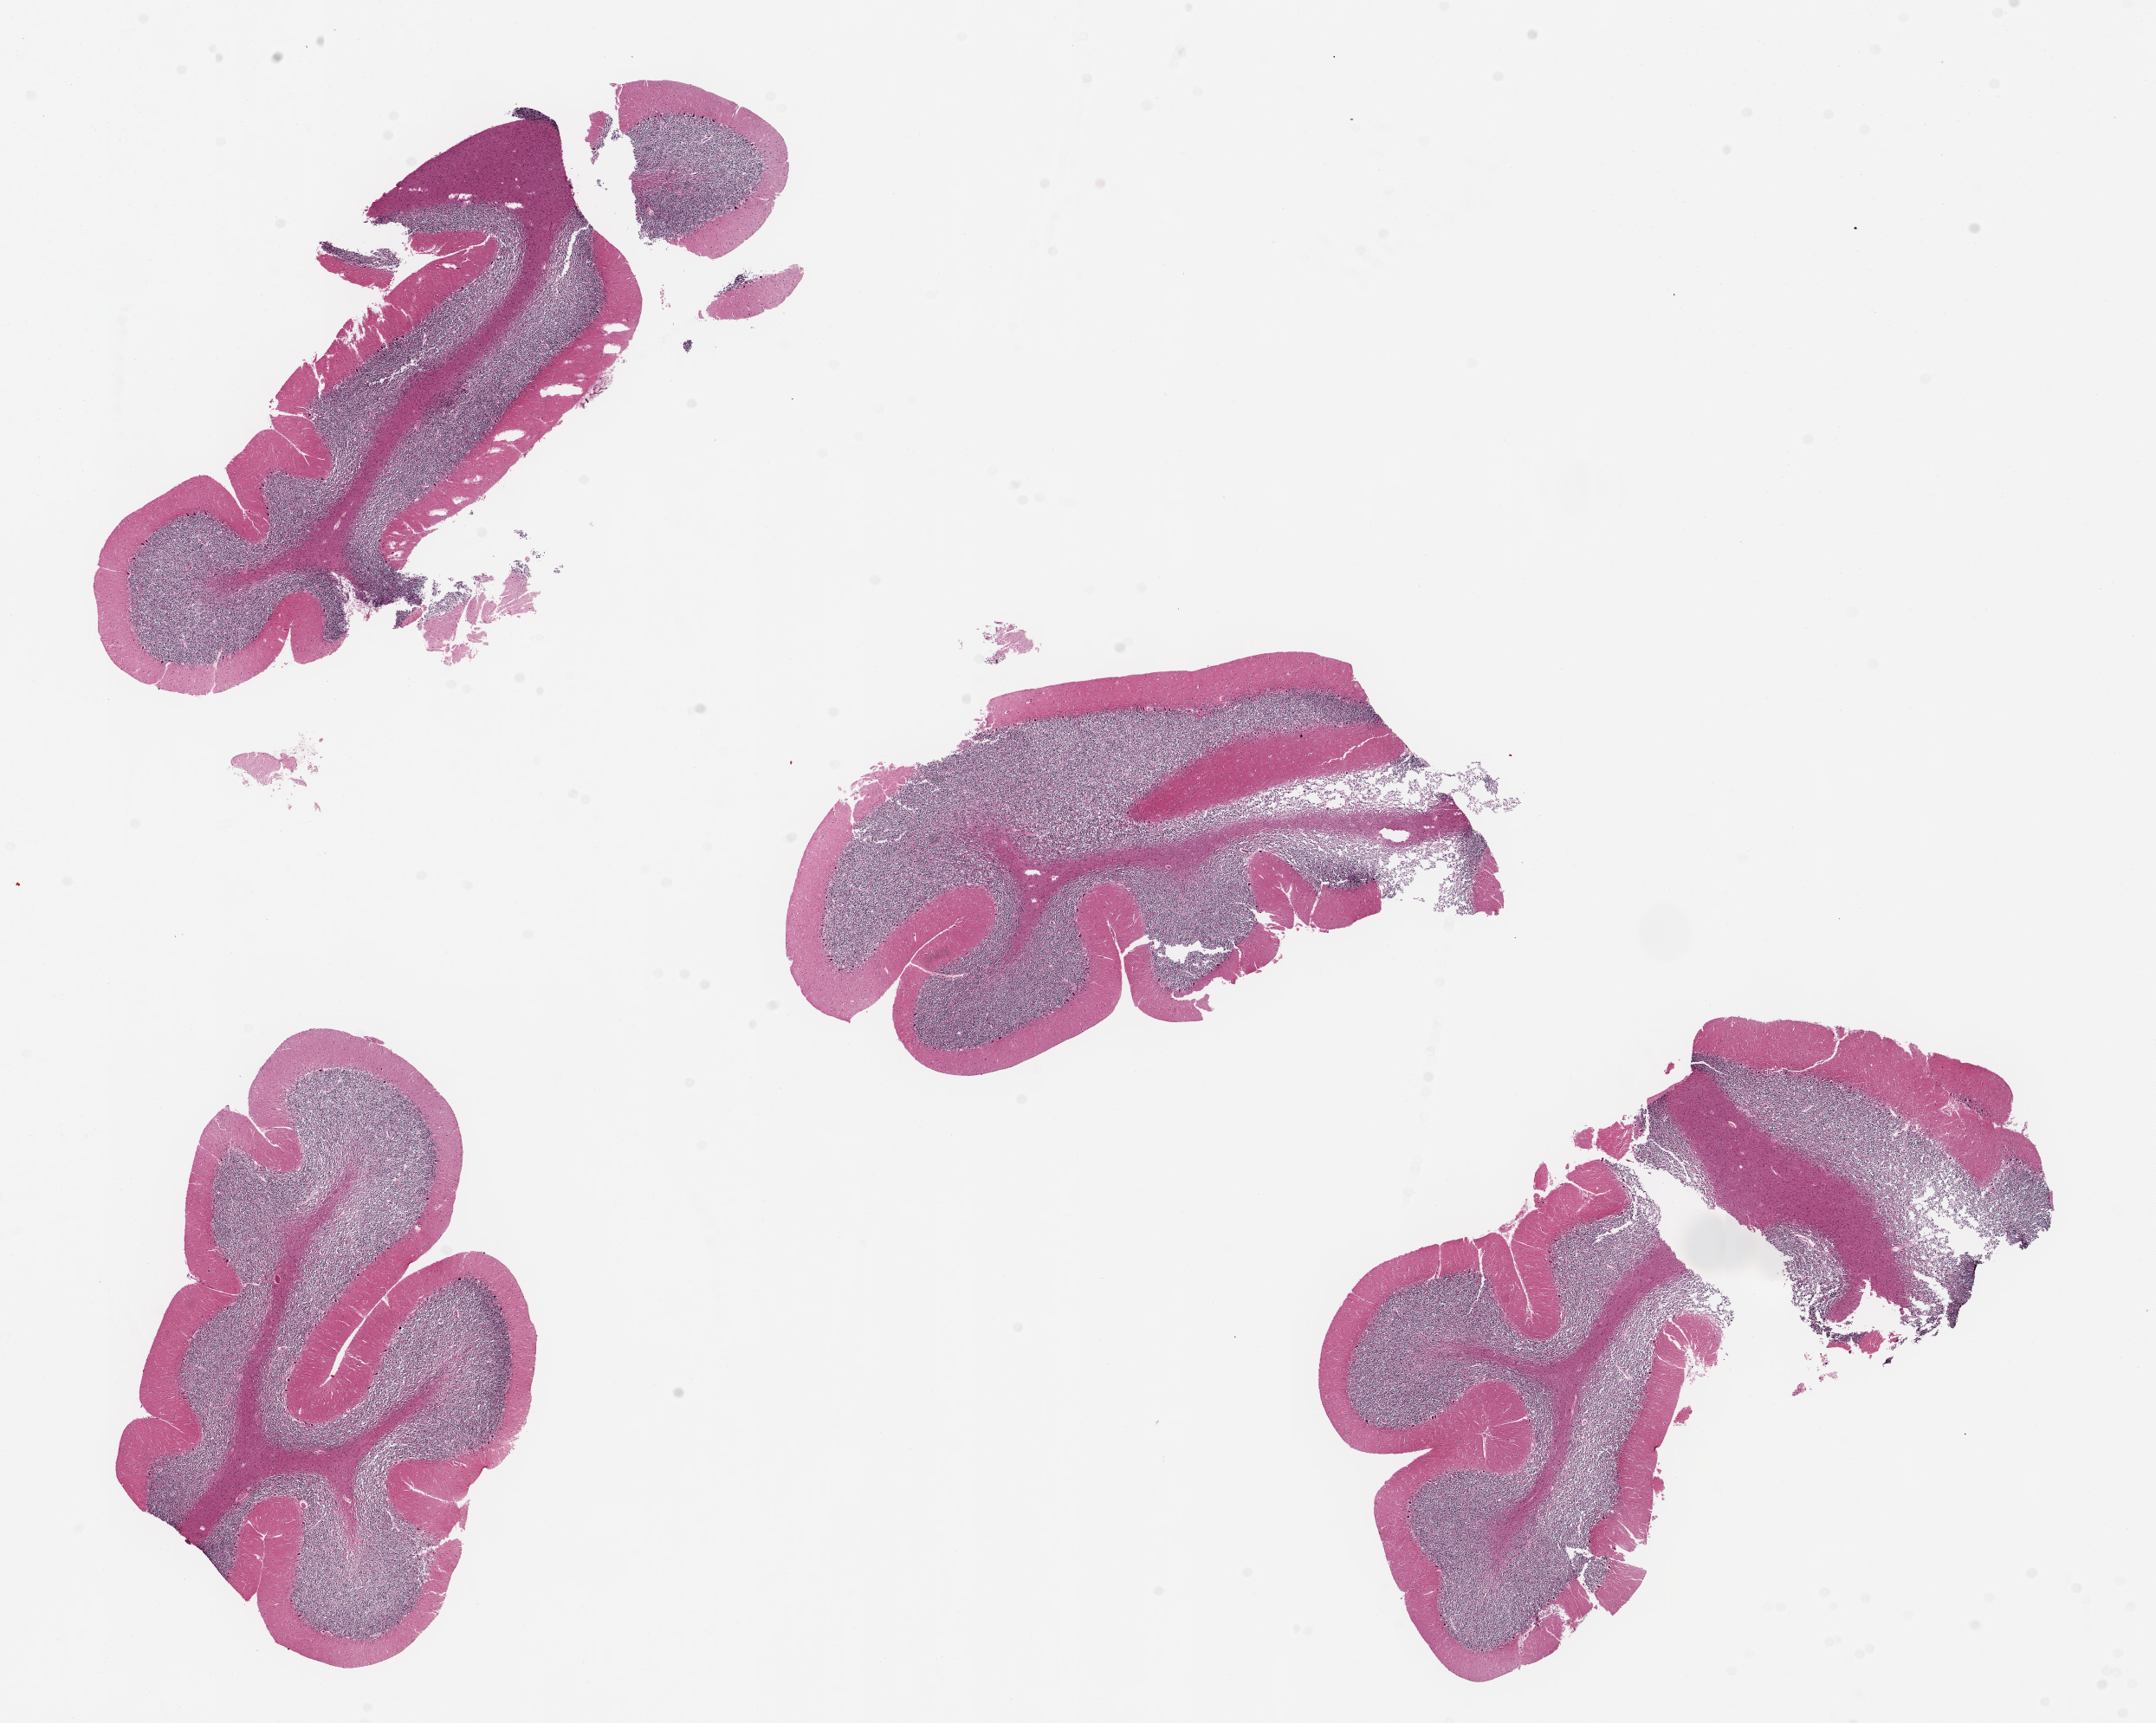
Whole-slide image, H&E stain, low-resolution overview of the scanned area, about 19.7 x 15.7 mm. PAXgene-fixed, paraffin-embedded tissue. Sampled site (target tissue): cerebellum. Donor tissue sample. Male donor.
Reviewer comment on this tissue sample: 4 ~ 6x3mm pieces. Granular layer more autolyzed.